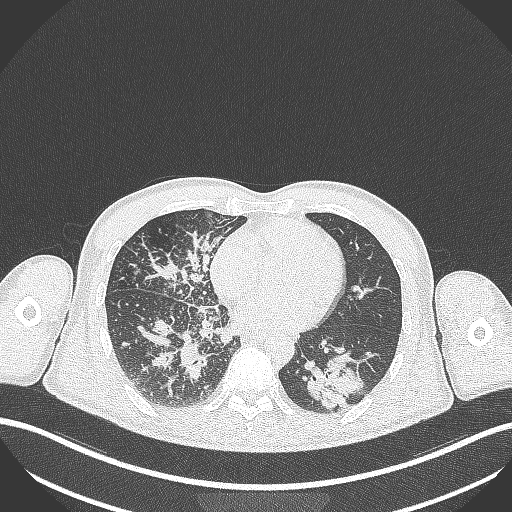
Chest CT, one axial slice; slice 124 of 348 in the series (ordered by position); 120 kVp; lung window (W 1500 / L -600 HU); 1 mm slice thickness; 512 × 512 image matrix, field of view 400 × 400 mm. Patient: male, 49 years. Case-level facts recorded for this patient, not image findings: clinical TNM (as recorded): T2b N1 M0.
Annotated regions visible in this slice (bounding box drawn by a radiologist):
- lung tumour (recorded histology: adenocarcinoma): bounding box [x1, y1, x2, y2] px = [297, 354, 369, 411]